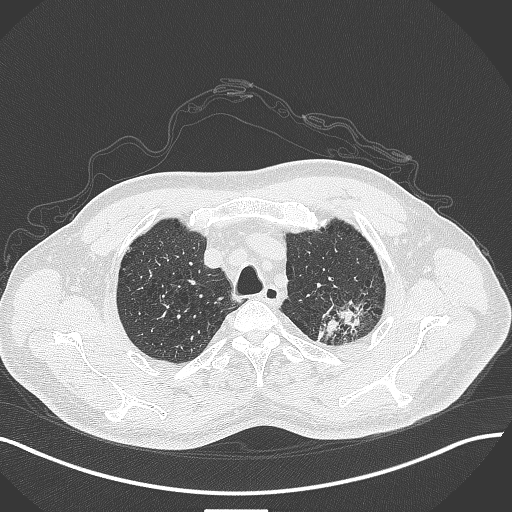
Chest CT, one axial slice. Position 354 of 429 along the scan axis. Reconstruction kernel B70f. Lung window (W 1500 / L -600 HU). 1 mm slice thickness. 512 × 512 image matrix, field of view 400 × 400 mm. Male patient, age 55 years. Case-level facts recorded for this patient, not image findings: clinical TNM (as recorded): T3 N0 M1c.
Outlined on this slice (rectangle marked by the reading radiologist):
- lung tumour (recorded histology: adenocarcinoma): bounding box (x1, y1, x2, y2) in pixels: (317, 292, 395, 358)